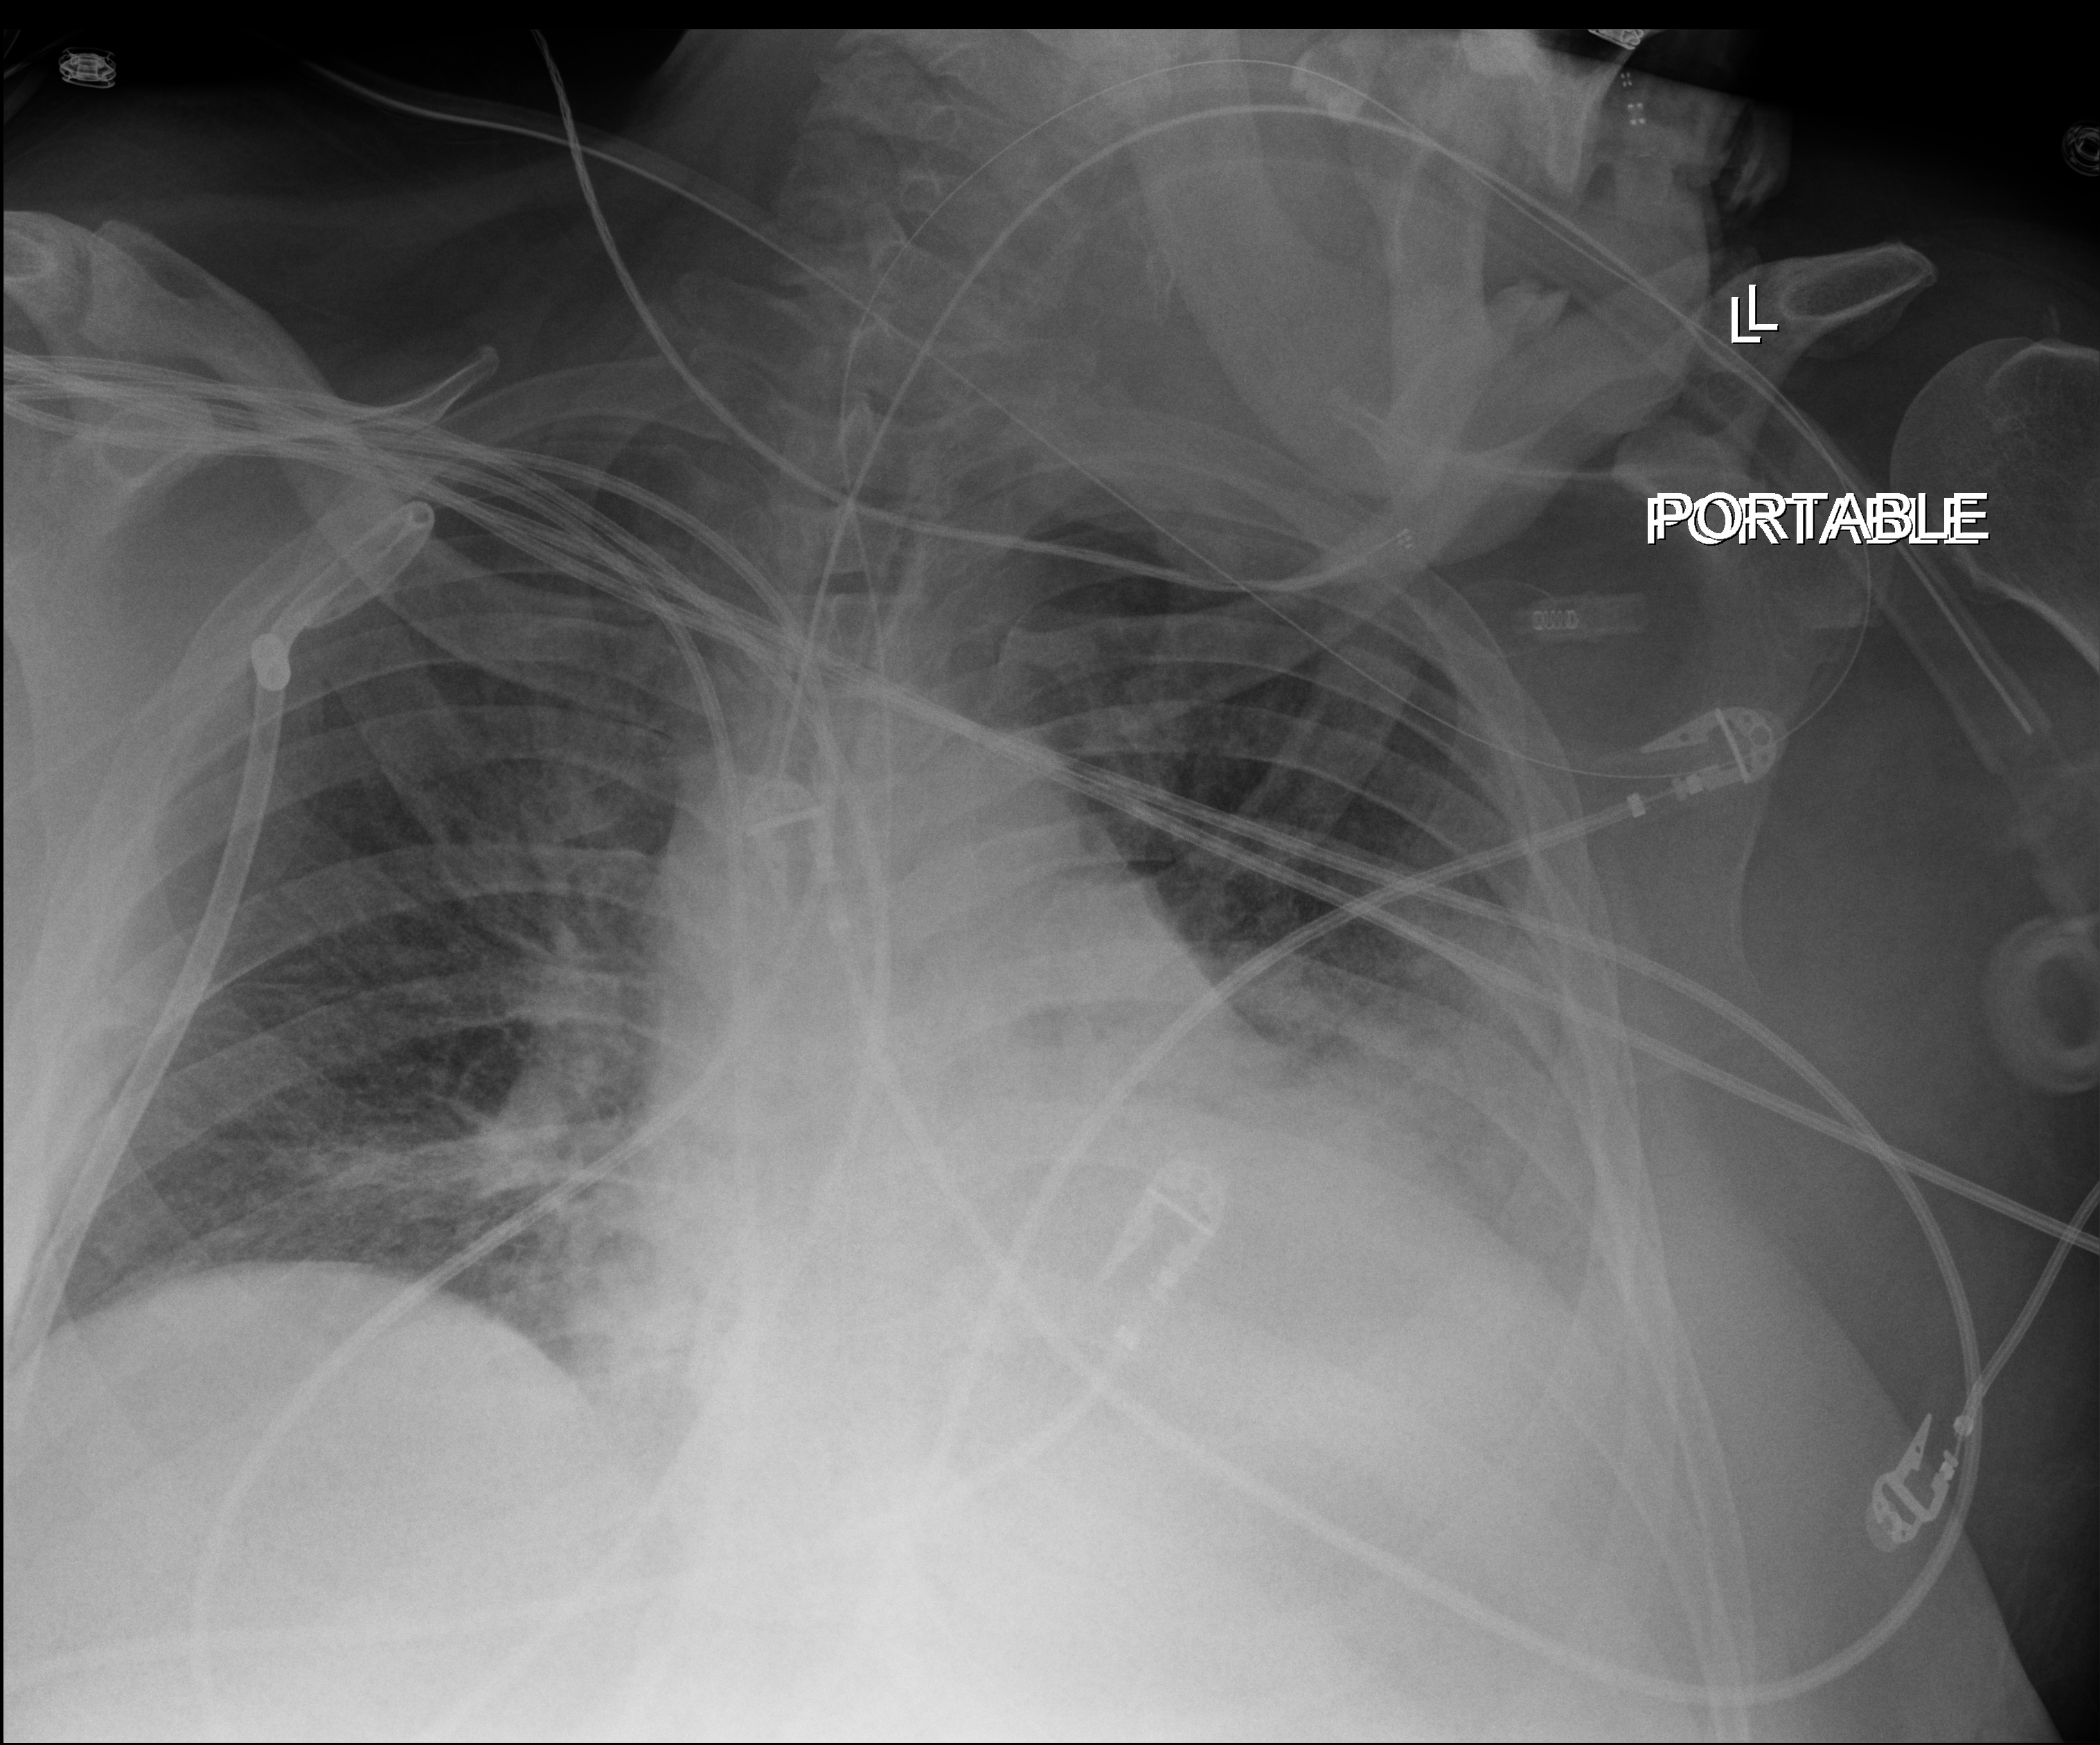
Chest radiograph, anteroposterior (AP) projection. Patient hospitalised with COVID-19; male, aged 60–74 years.
Admission-level facts for this patient (not findings on this image; timing relative to this image not recorded): admitted to intensive care during this hospital stay: yes; mechanically ventilated during this hospital stay: yes.